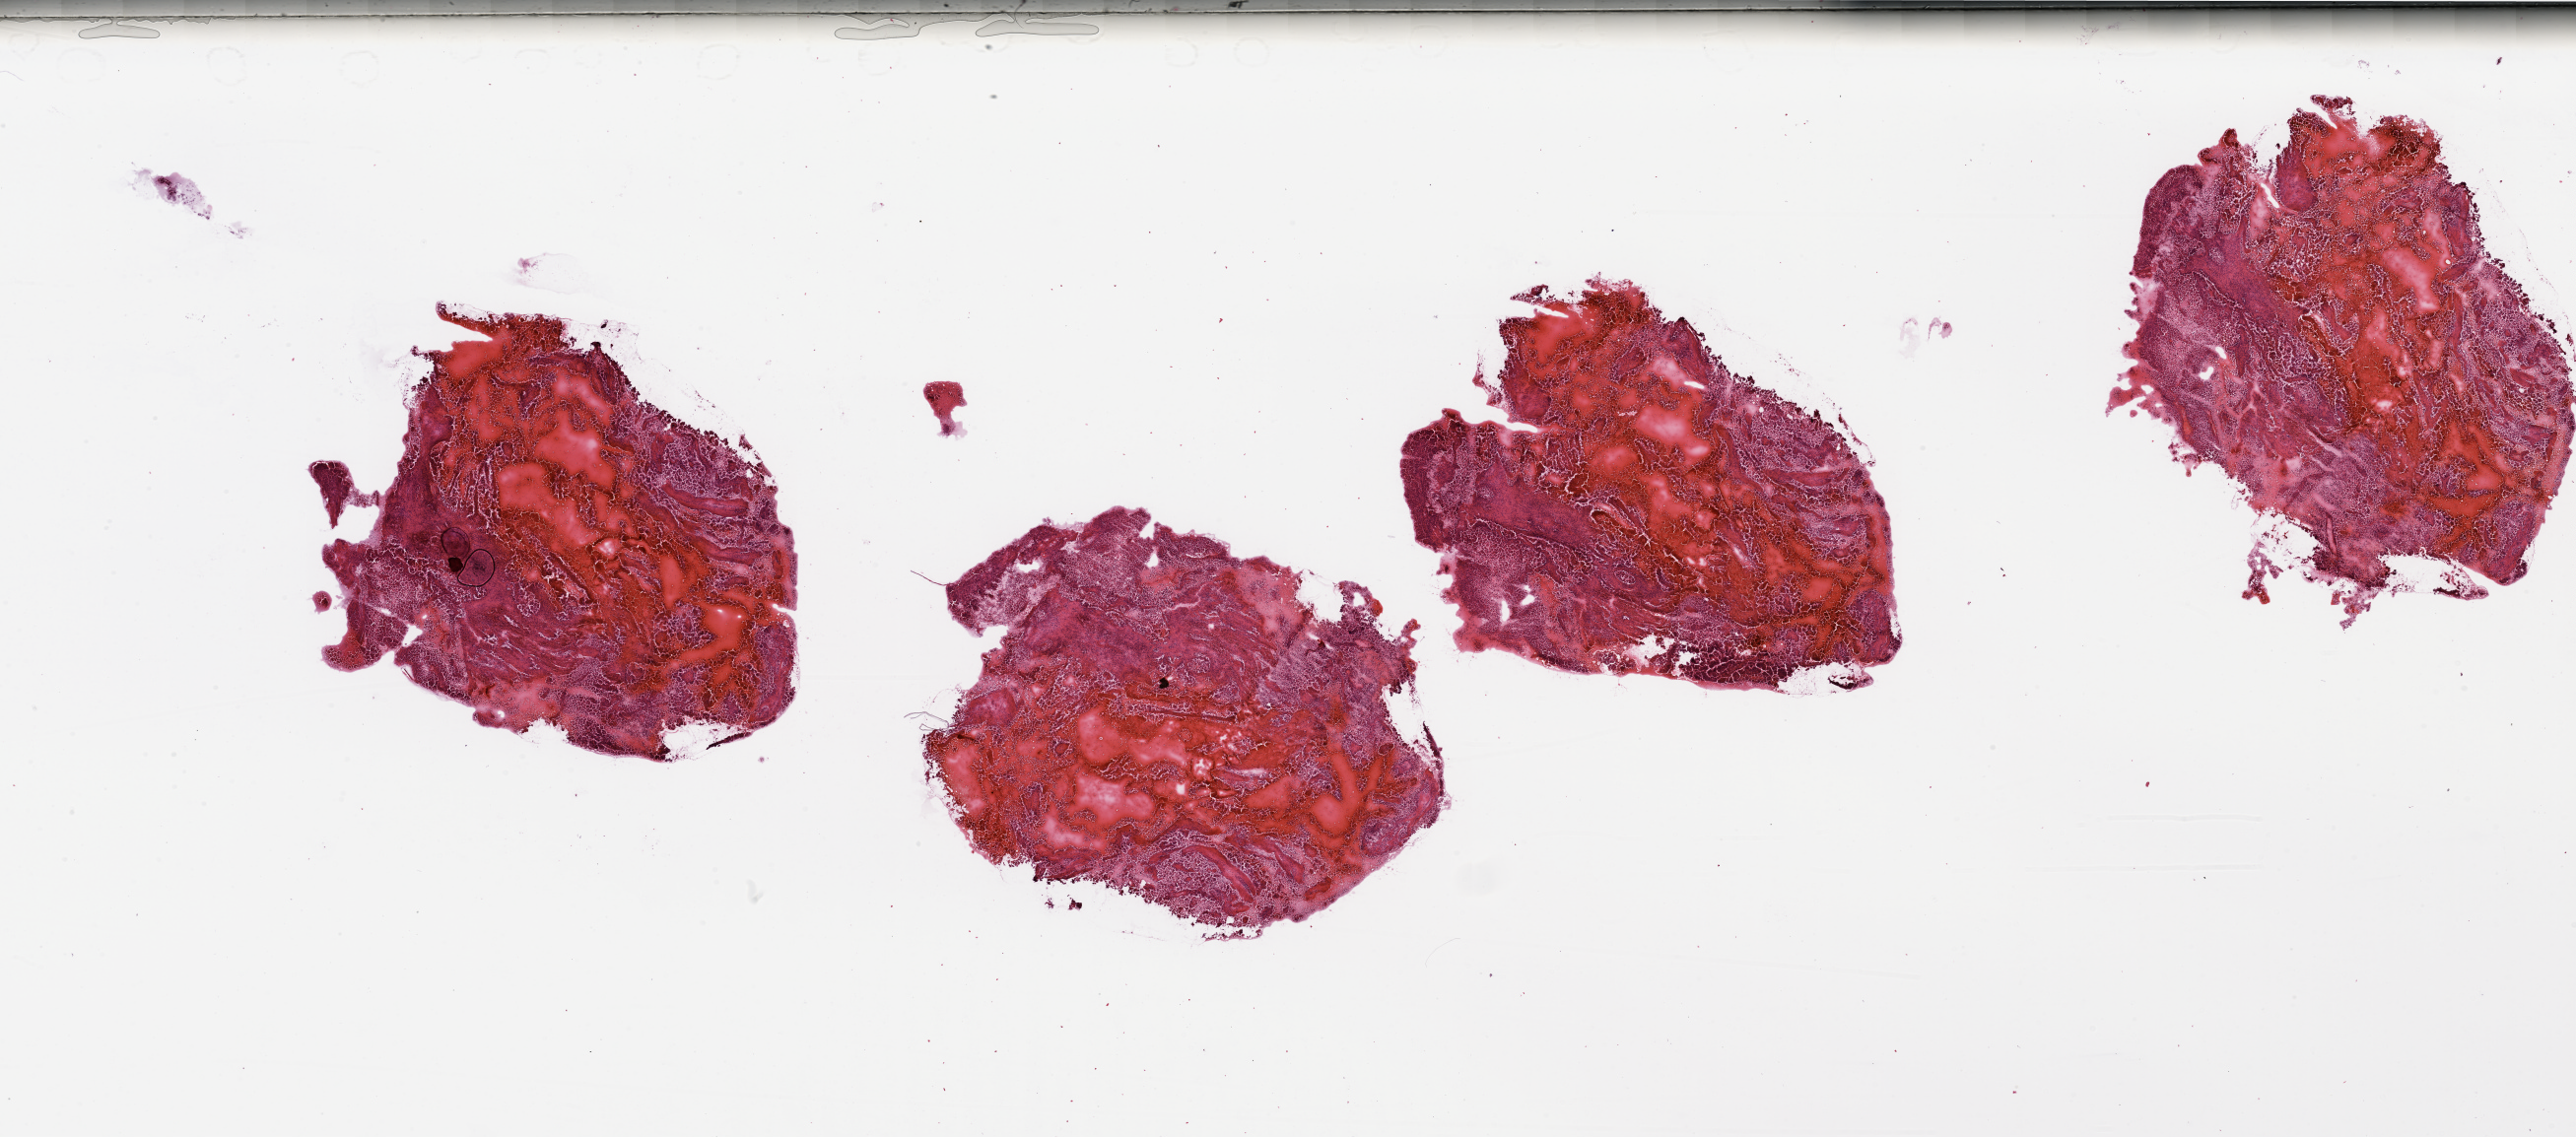
Digitized H&E tissue section (whole slide), shown as a low-resolution overview of the whole scanned area (about 41.3 x 18.3 mm). Tumour tissue sample, sampled site: kidney. Patient: female, age 74 years. Histologic grade: G2 (moderately differentiated). Composition of this section per pathologist review: tumour nuclei 60%, necrosis 20%.
Diagnosis: Renal cell carcinoma, NOS. Primary tumour site (as recorded): lower pole. AJCC pathologic stage: I.